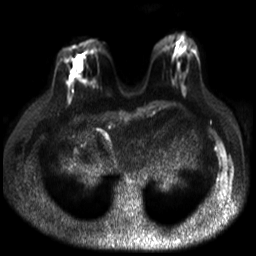
Breast MRI, one axial slice. Slice 10 of 30 in the series (ordered by position). Diffusion-weighted series; image 2 of 4 stored at this slice position (different b-values; order by instance number). 3 T. 4 mm slice thickness. 256 × 256 image matrix, field of view 320 × 320 mm. Female patient.
Outlined on this slice (expert manual segmentation):
- tumour on diffusion-weighted imaging: box from (x=70, y=66) to (x=82, y=86) px